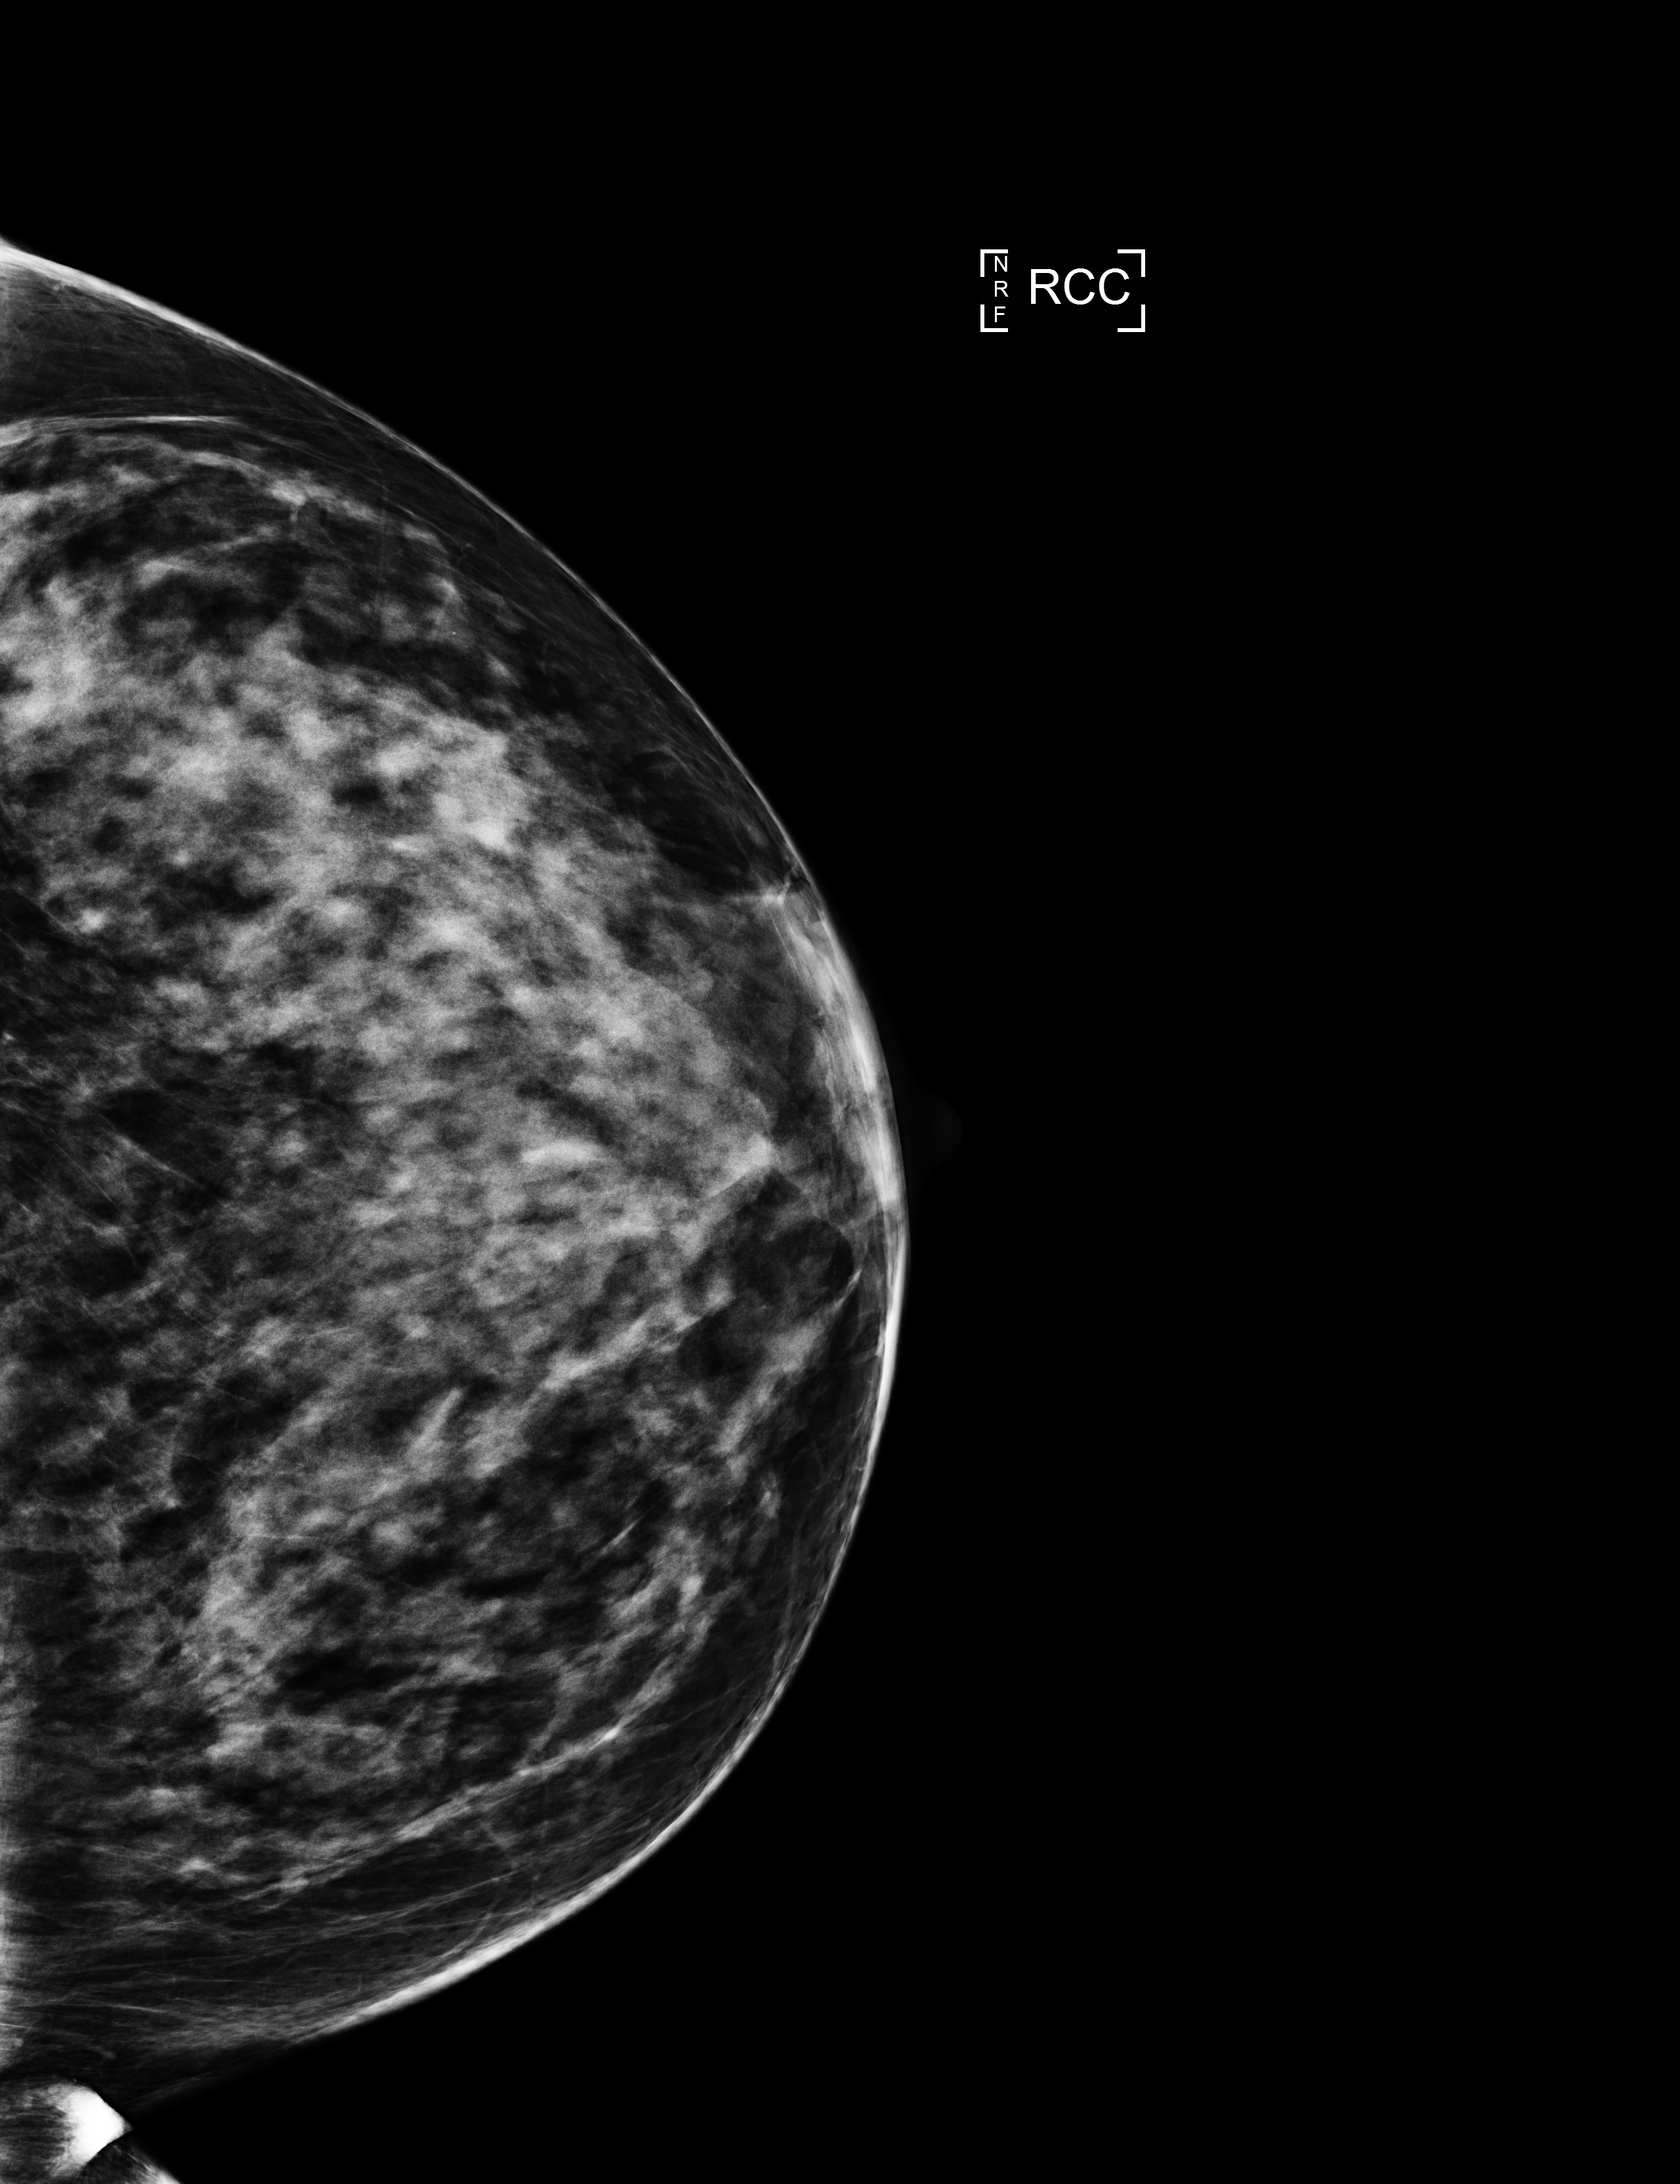
Full-field digital mammogram (FFDM), right breast, CC view, annual screening mammography examination, compressed breast thickness 68 mm. Patient aged 60 years (female).
BI-RADS breast density category at the screening exam (both breasts, scale 1–4): 4. Final BI-RADS assessment for this screening round (tomosynthesis exam, both breasts): category 1. Recall: no recall after this screen.